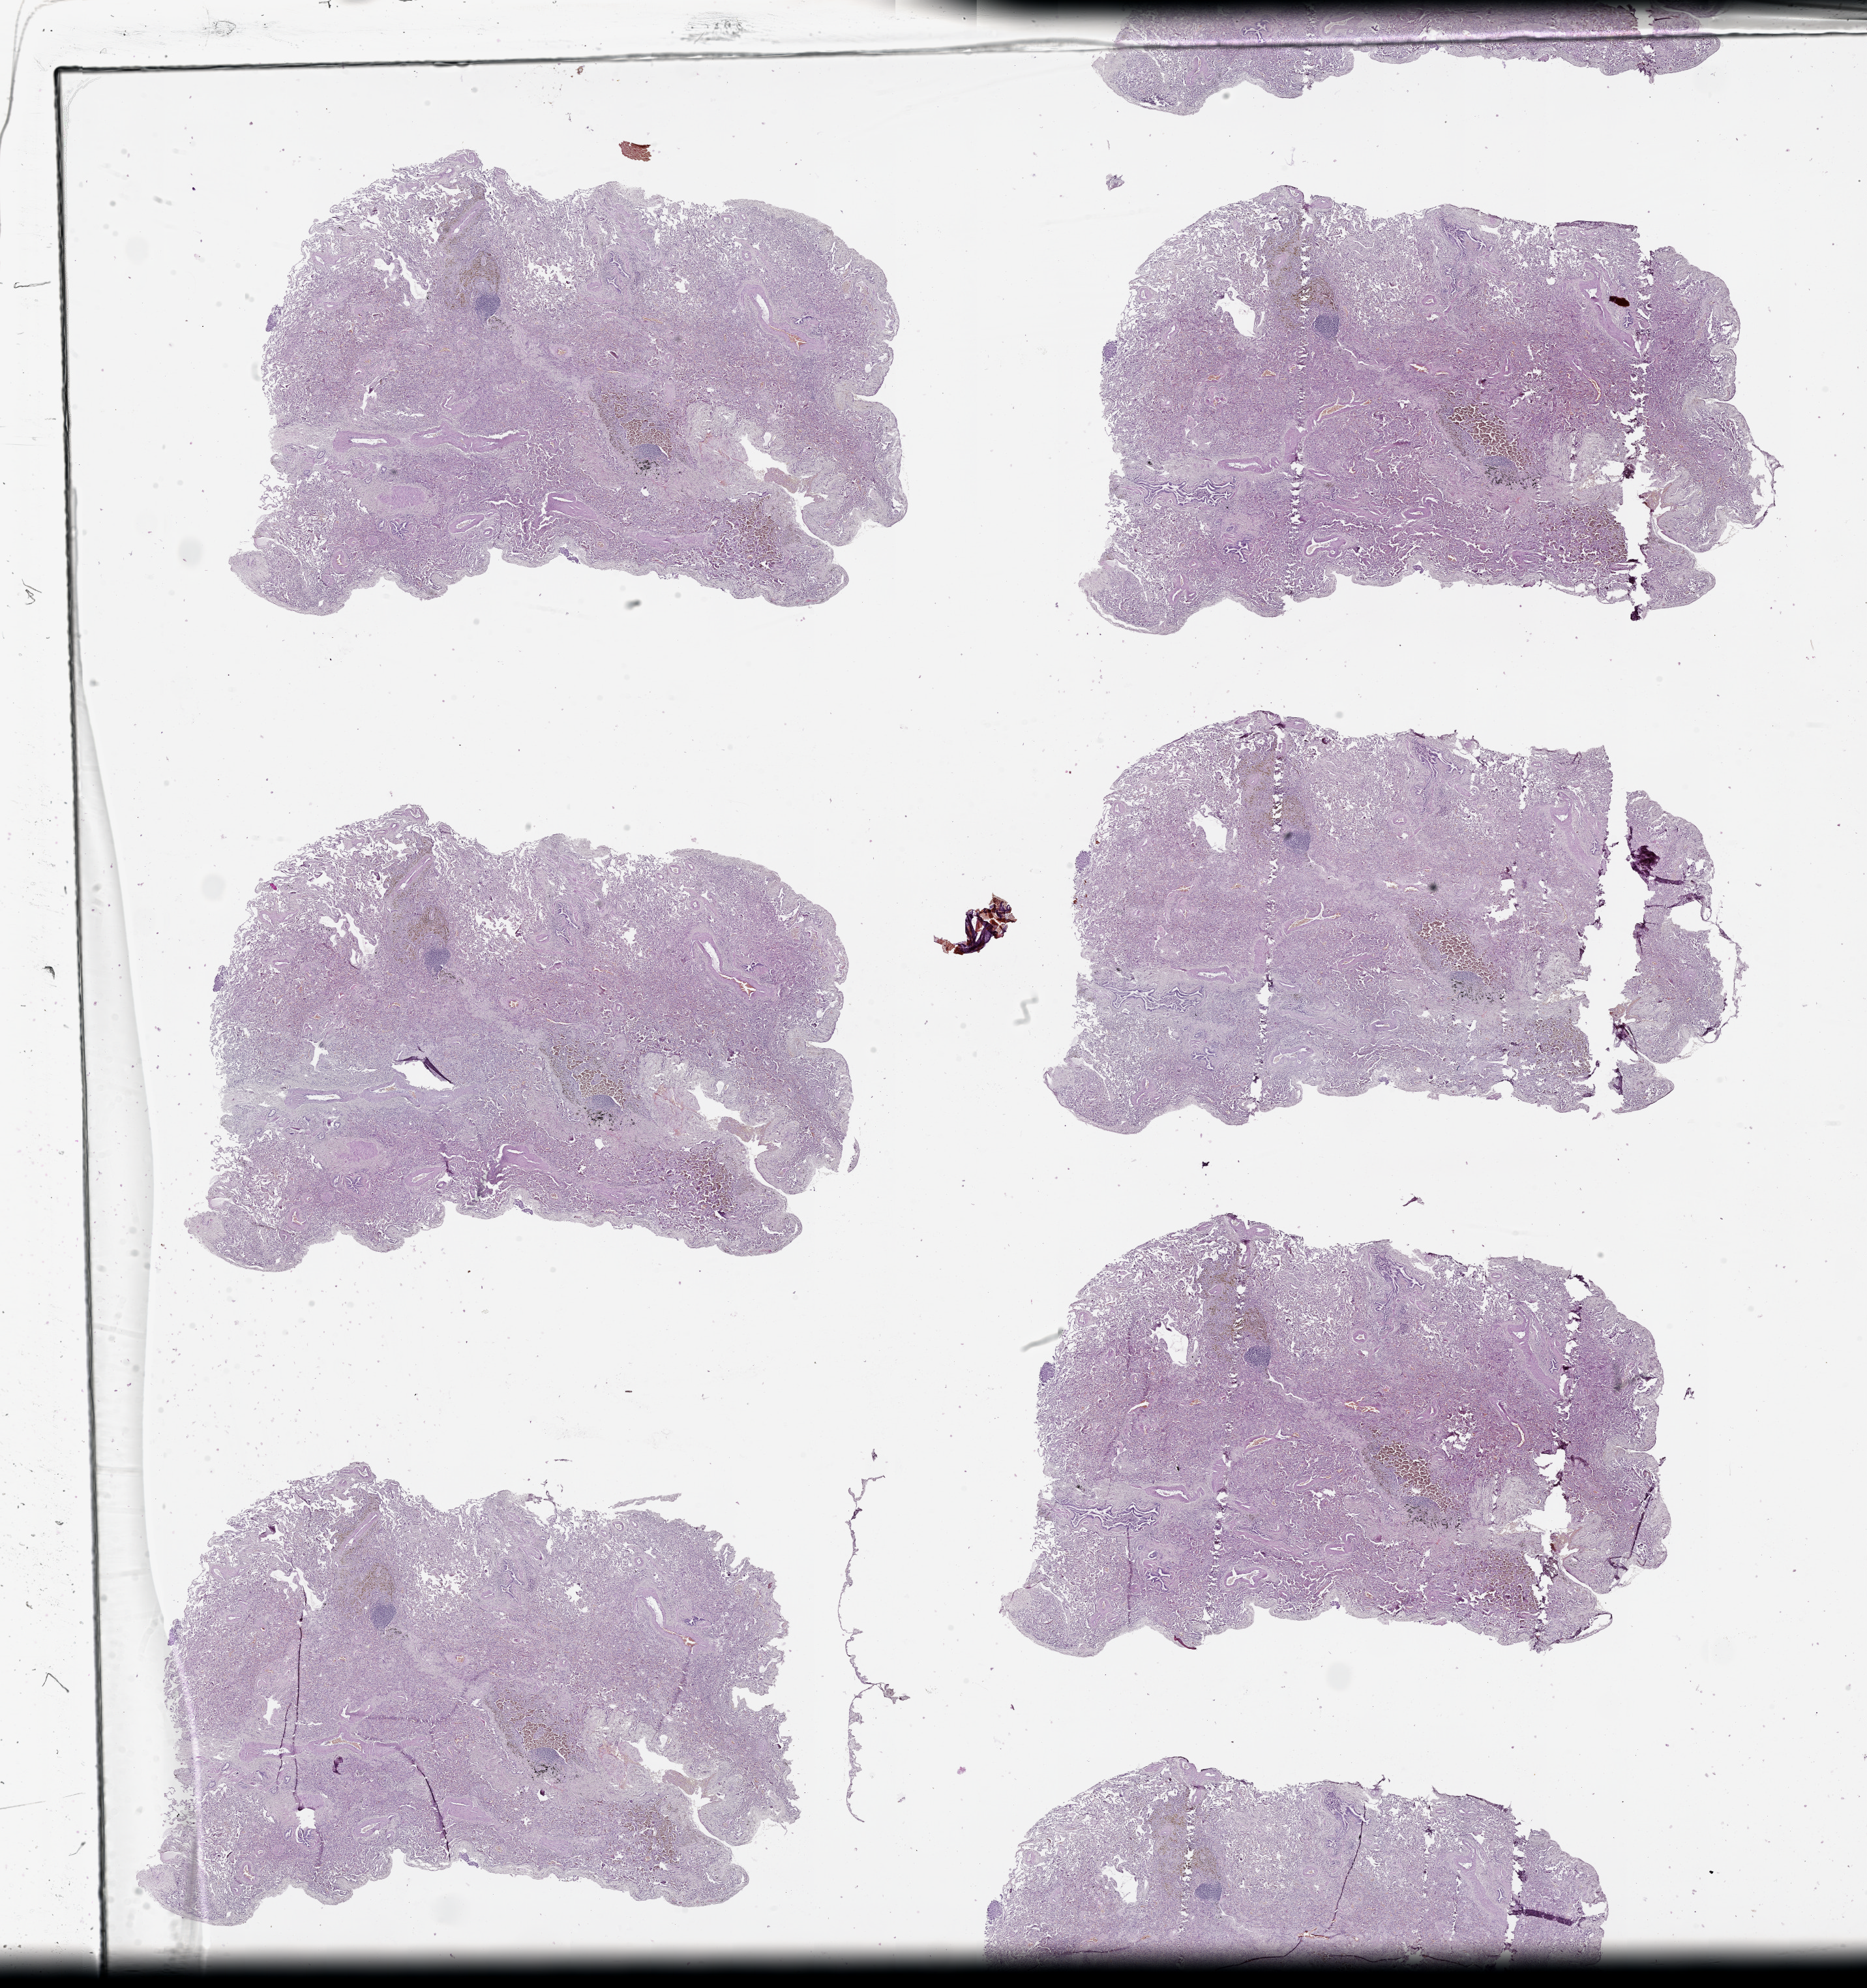
H&E-stained whole-slide image — shown as a low-resolution overview of the whole scanned area (about 23.1 x 24.5 mm, from a 20x scan); lung, tissue type not recorded.
Patient diagnosis (cohort enrolment): lung adenocarcinoma (lung).